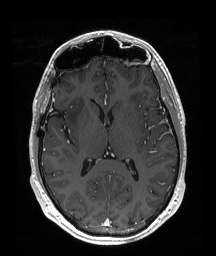
Brain MRI from a brain-tumour surgery series, one axial slice. Slice 100 of 192 in the series (ordered by position). T1-weighted post-contrast. 1 mm slice thickness. 216 × 256 image matrix, field of view 219 × 260 mm. Case-level facts recorded for this patient, not image findings: histopathology: Astrocytoma; WHO grade: 2; IDH mutation: yes.
Outlined on this slice (manually delineated by an expert):
- tumour: box from (x=66, y=97) to (x=85, y=127) px